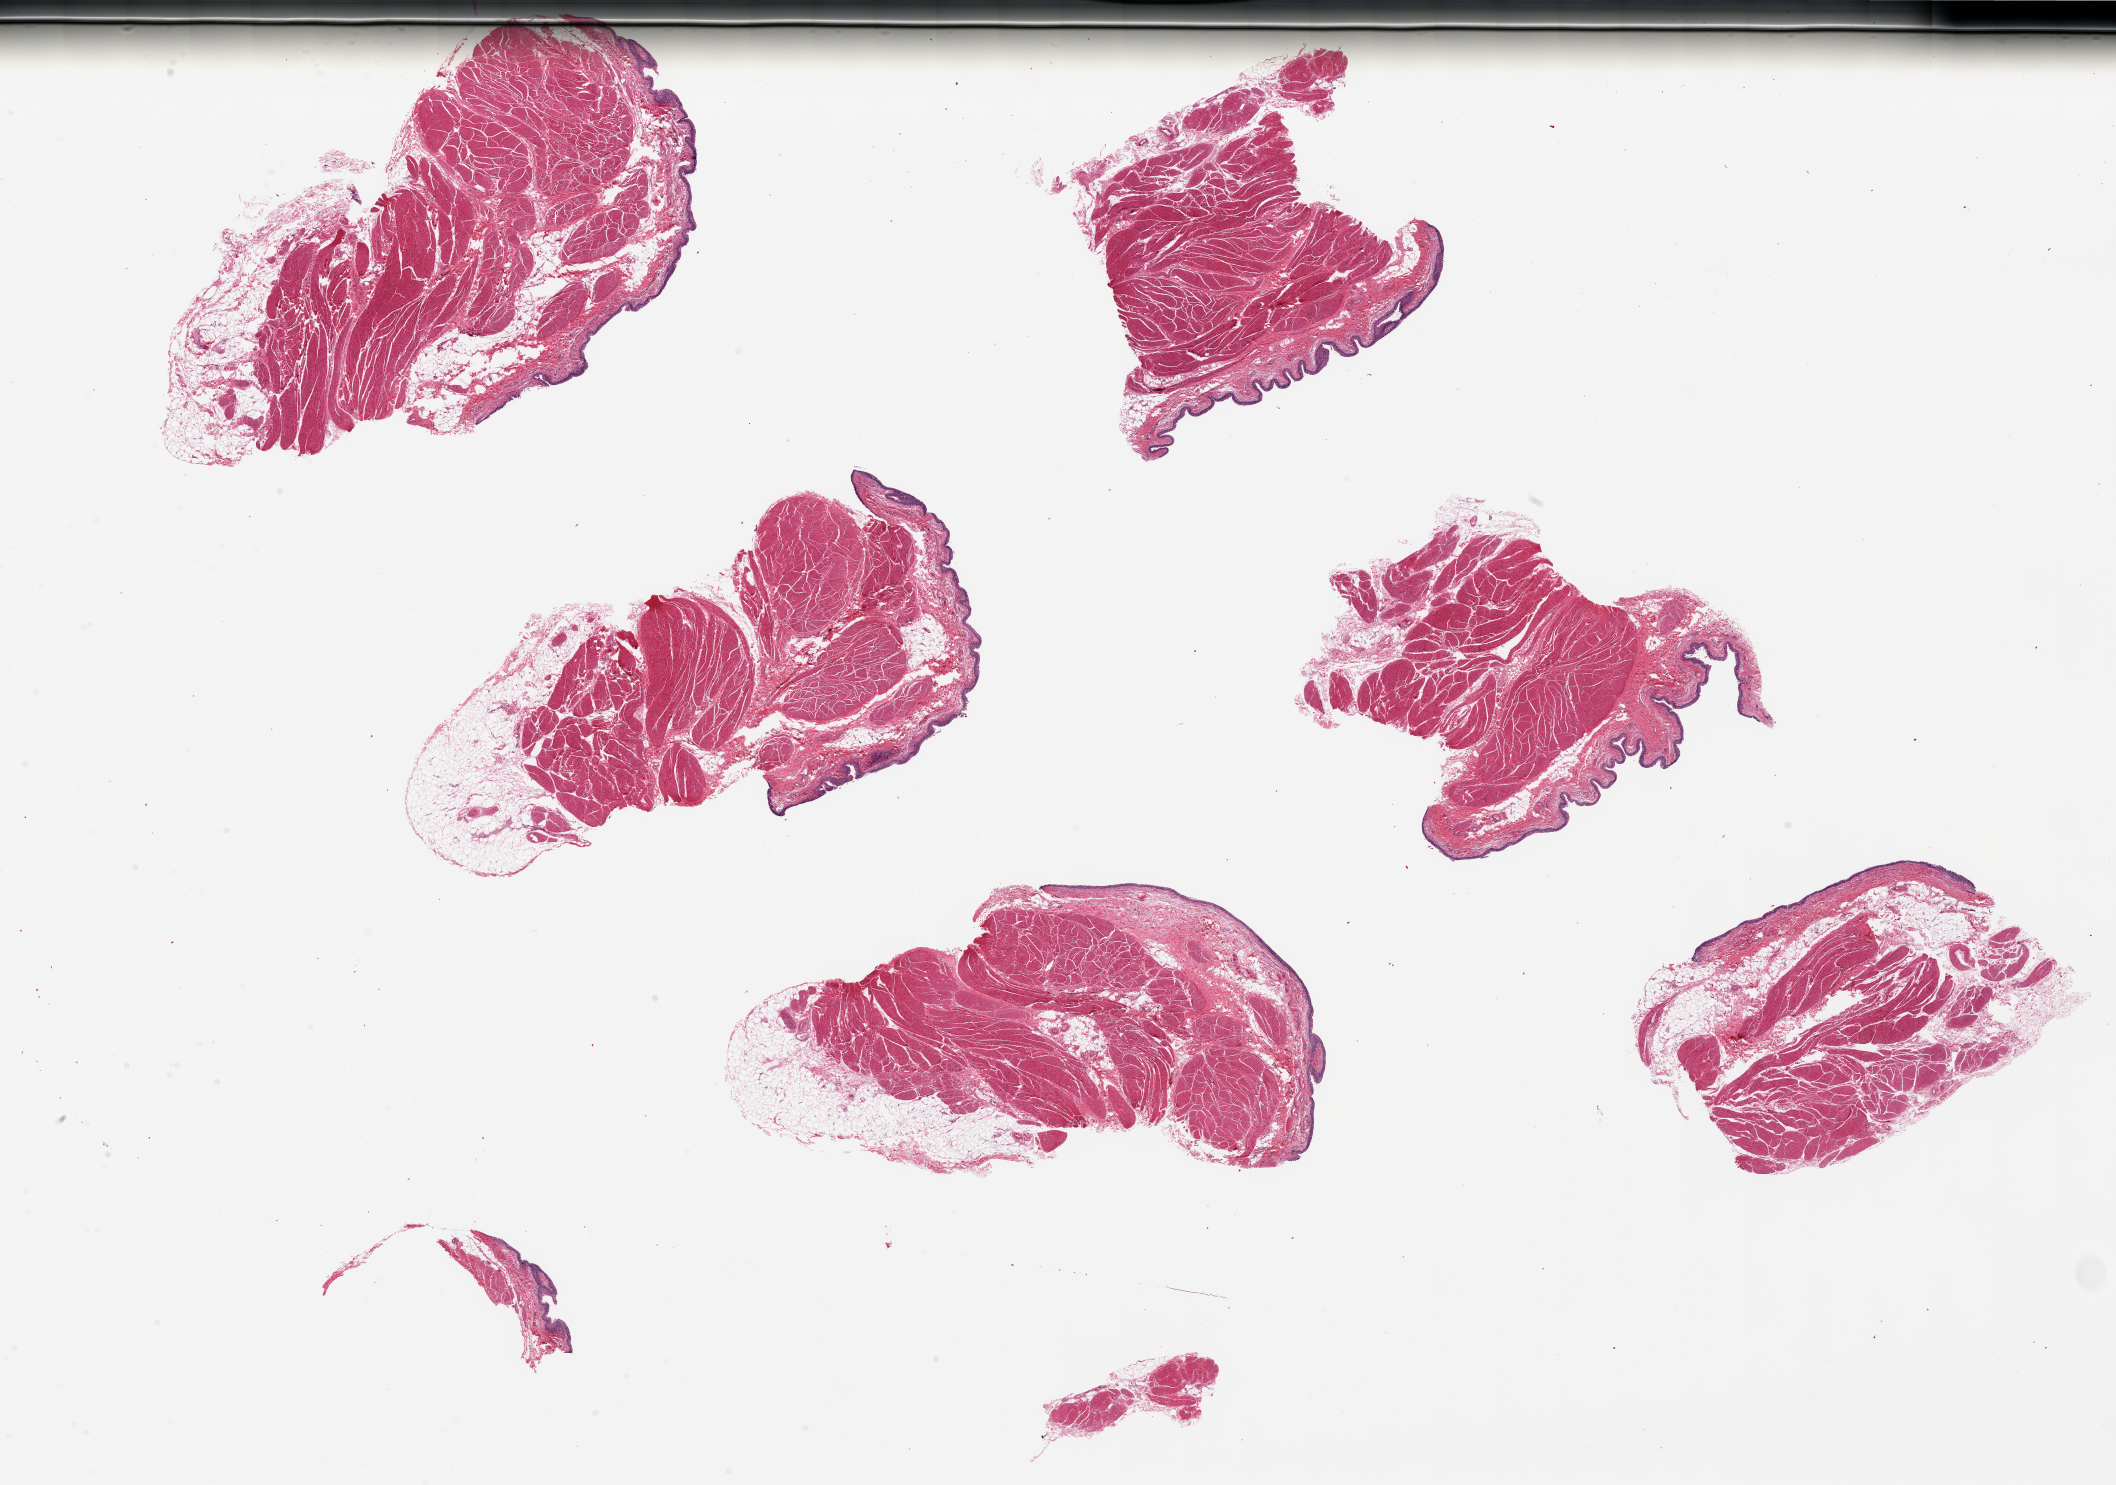
Digitized hematoxylin and eosin (H&E)-stained section, low-resolution overview of the scanned area, about 33.5 x 23.5 mm (slide scanned at 20x); PAXgene-fixed, paraffin-embedded tissue; sampled site (target tissue): urinary bladder; tissue donor sample. Male donor.
Reviewer comment on this tissue sample: 6 ~6x4mm pieces. Urothelium well-preserved, 0.5-1% of specimen thickness.